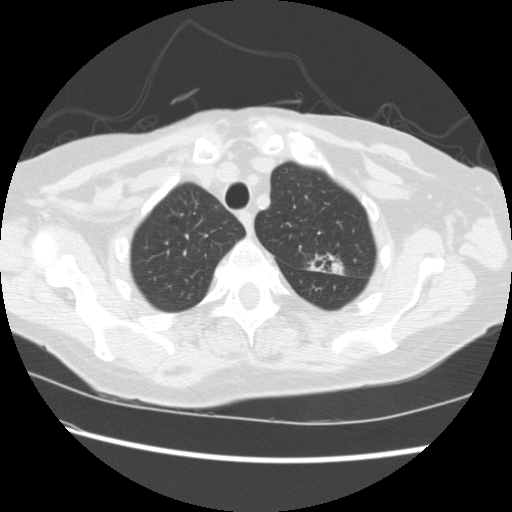
Low-dose screening chest CT, one axial slice. Position 184 of 224 along the scan axis. Reconstruction kernel STANDARD. 120 kVp. Lung window (W 1500 / L -600 HU). 2.5 mm slice thickness. 512 × 512 image matrix, field of view 340 × 340 mm.
Annotated regions visible in this slice (manually delineated by an expert):
- lesion 1 (tumor, upper lobe of left lung): bounding box [x1, y1, x2, y2] px = [330, 262, 344, 275]